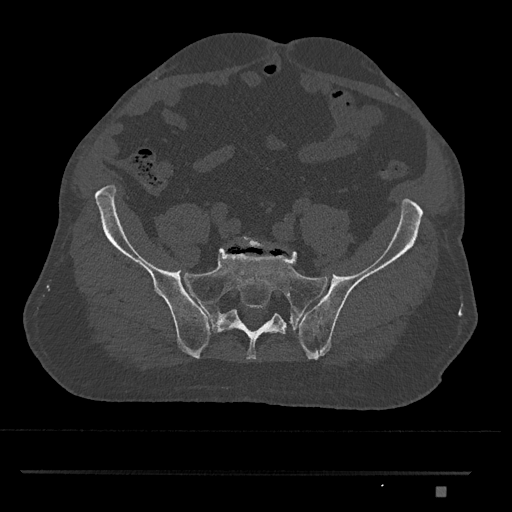
CT including the spine, one axial slice; position 493 of 1134 along the scan axis; 120 kVp; bone window (W 1800 / L 400 HU); 0.5 mm slice thickness; 512 × 512 image matrix, field of view 429 × 429 mm. Patient: male, 65 years. From the clinical record (not read from this slice): primary cancer: prostate.
Outlined on this slice (semi-automatically segmented with operator editing):
- L5 vertebra: bounding box [x1, y1, x2, y2] px = [239, 236, 278, 249]